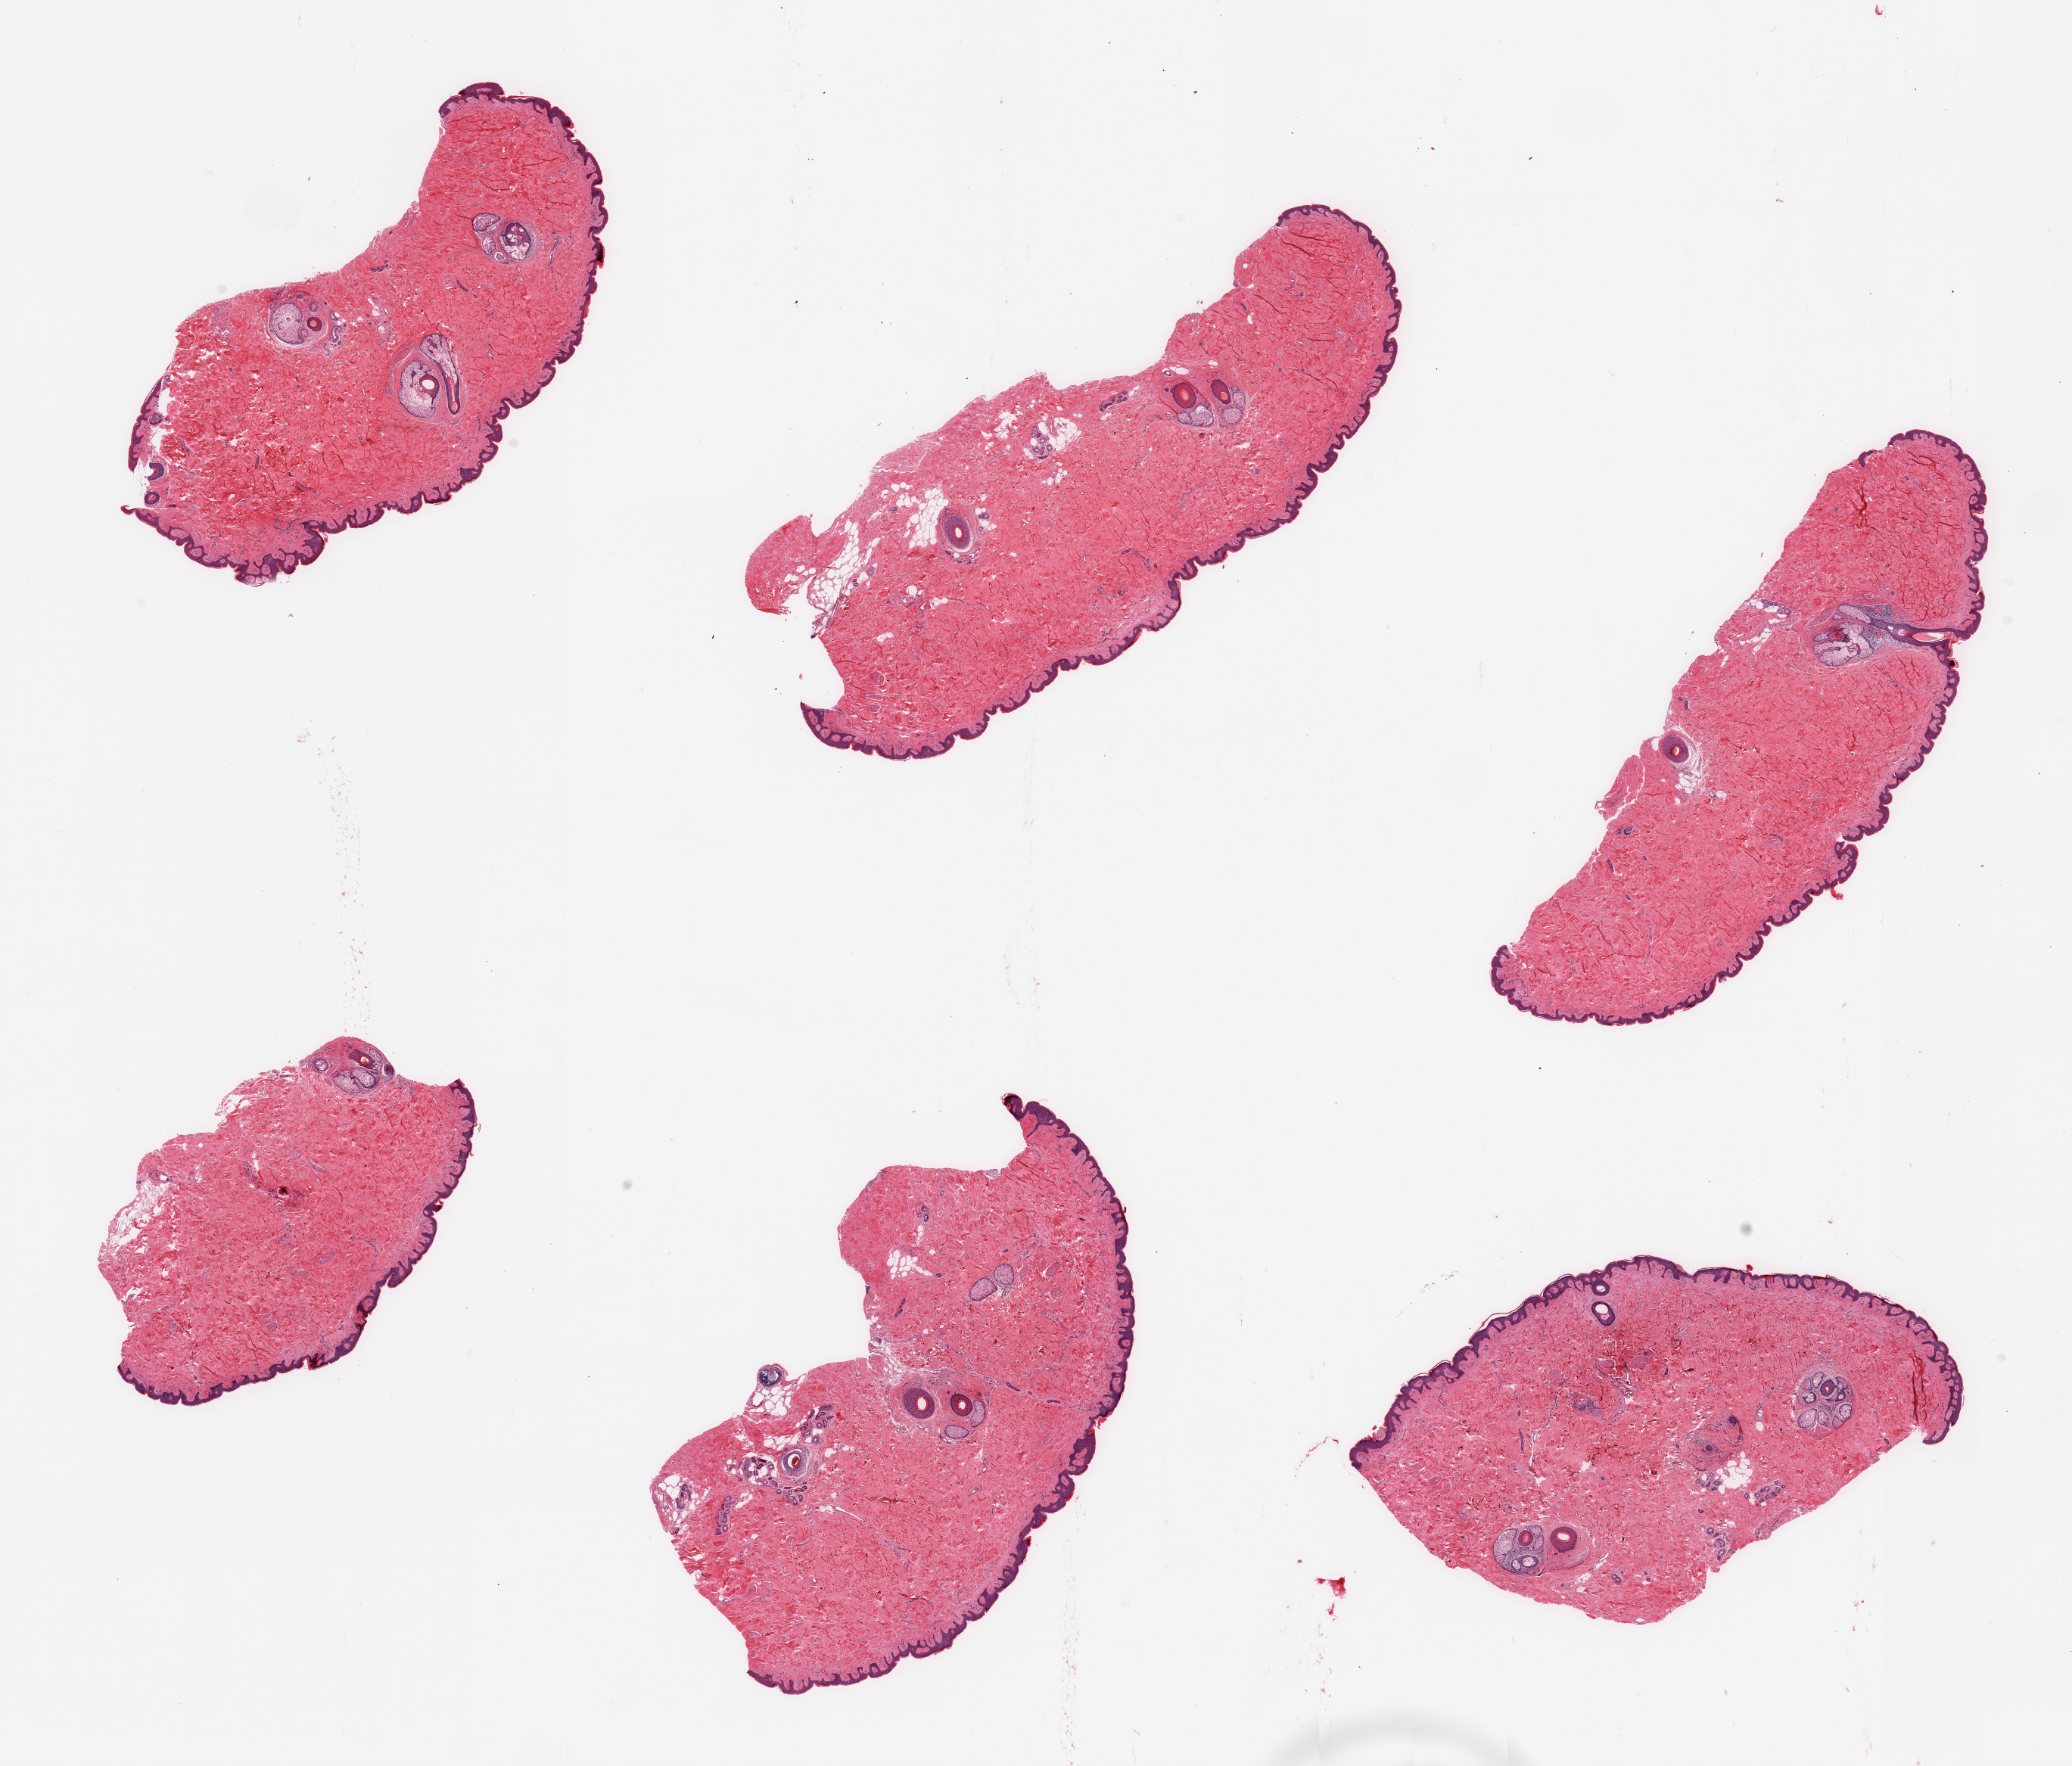
Whole-slide image, haematoxylin and eosin stain — a low-resolution overview of the entire scanned area, about 21.7 x 18.5 mm, PAXgene-fixed, paraffin-embedded tissue, section of skin of suprapubic region (target tissue), tissue donor sample. Donor: male.
Reviewer comment on this tissue sample: 6 pieces; well trimmed with insignificant periadnexal fat.